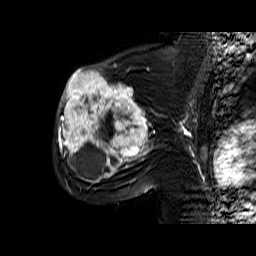
Breast MRI (dynamic contrast-enhanced), one sagittal slice. Slice 38 of 60 in the series (ordered by position). Dynamic contrast-enhanced series, time point 2 of 6 at this slice position (early post-contrast). 1.5 T. TE 6.4 ms, TR 32.9 ms. 256 × 256 image matrix, field of view 200 × 200 mm. Female patient. Case-level facts recorded for this patient, not image findings: setting: breast cancer imaged before/during neoadjuvant chemotherapy; receptor status: triple-negative.
Outlined on this slice (semi-automatically segmented with operator editing):
- analysis volume of interest (the breast-tissue region the enhancement analysis was run in; not a lesion): bounding box (x1, y1, x2, y2) in pixels: (55, 65, 159, 174)
- tumour enhancement mask (voxels above the 100 % enhancement threshold inside the analysis volume of interest): (59, 69, 154, 174)